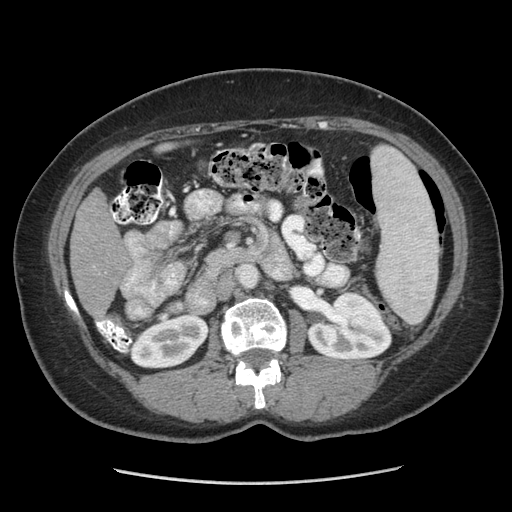
Contrast-enhanced abdominal CT (liver protocol), one axial slice; slice 124 of 185 in the series (ordered by position); reconstruction kernel STANDARD; 140 kVp; soft-tissue window (W 400 / L 40 HU); 512 × 512 image matrix, field of view 360 × 360 mm. Case-level facts recorded for this patient, not image findings: diagnosis: hepatocellular carcinoma (patient treated with transarterial chemoembolisation; whether this scan precedes or follows treatment is not stated here); TNM stage (as recorded): Stage-I; Child-Pugh class: A; tumour nodularity: uninodular.
Outlined on this slice (semi-automatic segmentation, software-assisted and operator-edited):
- liver parenchyma outside the tumour (the mass and vessels are separate outlines, so this box may not span the whole liver): box from (x=70, y=188) to (x=132, y=314) px